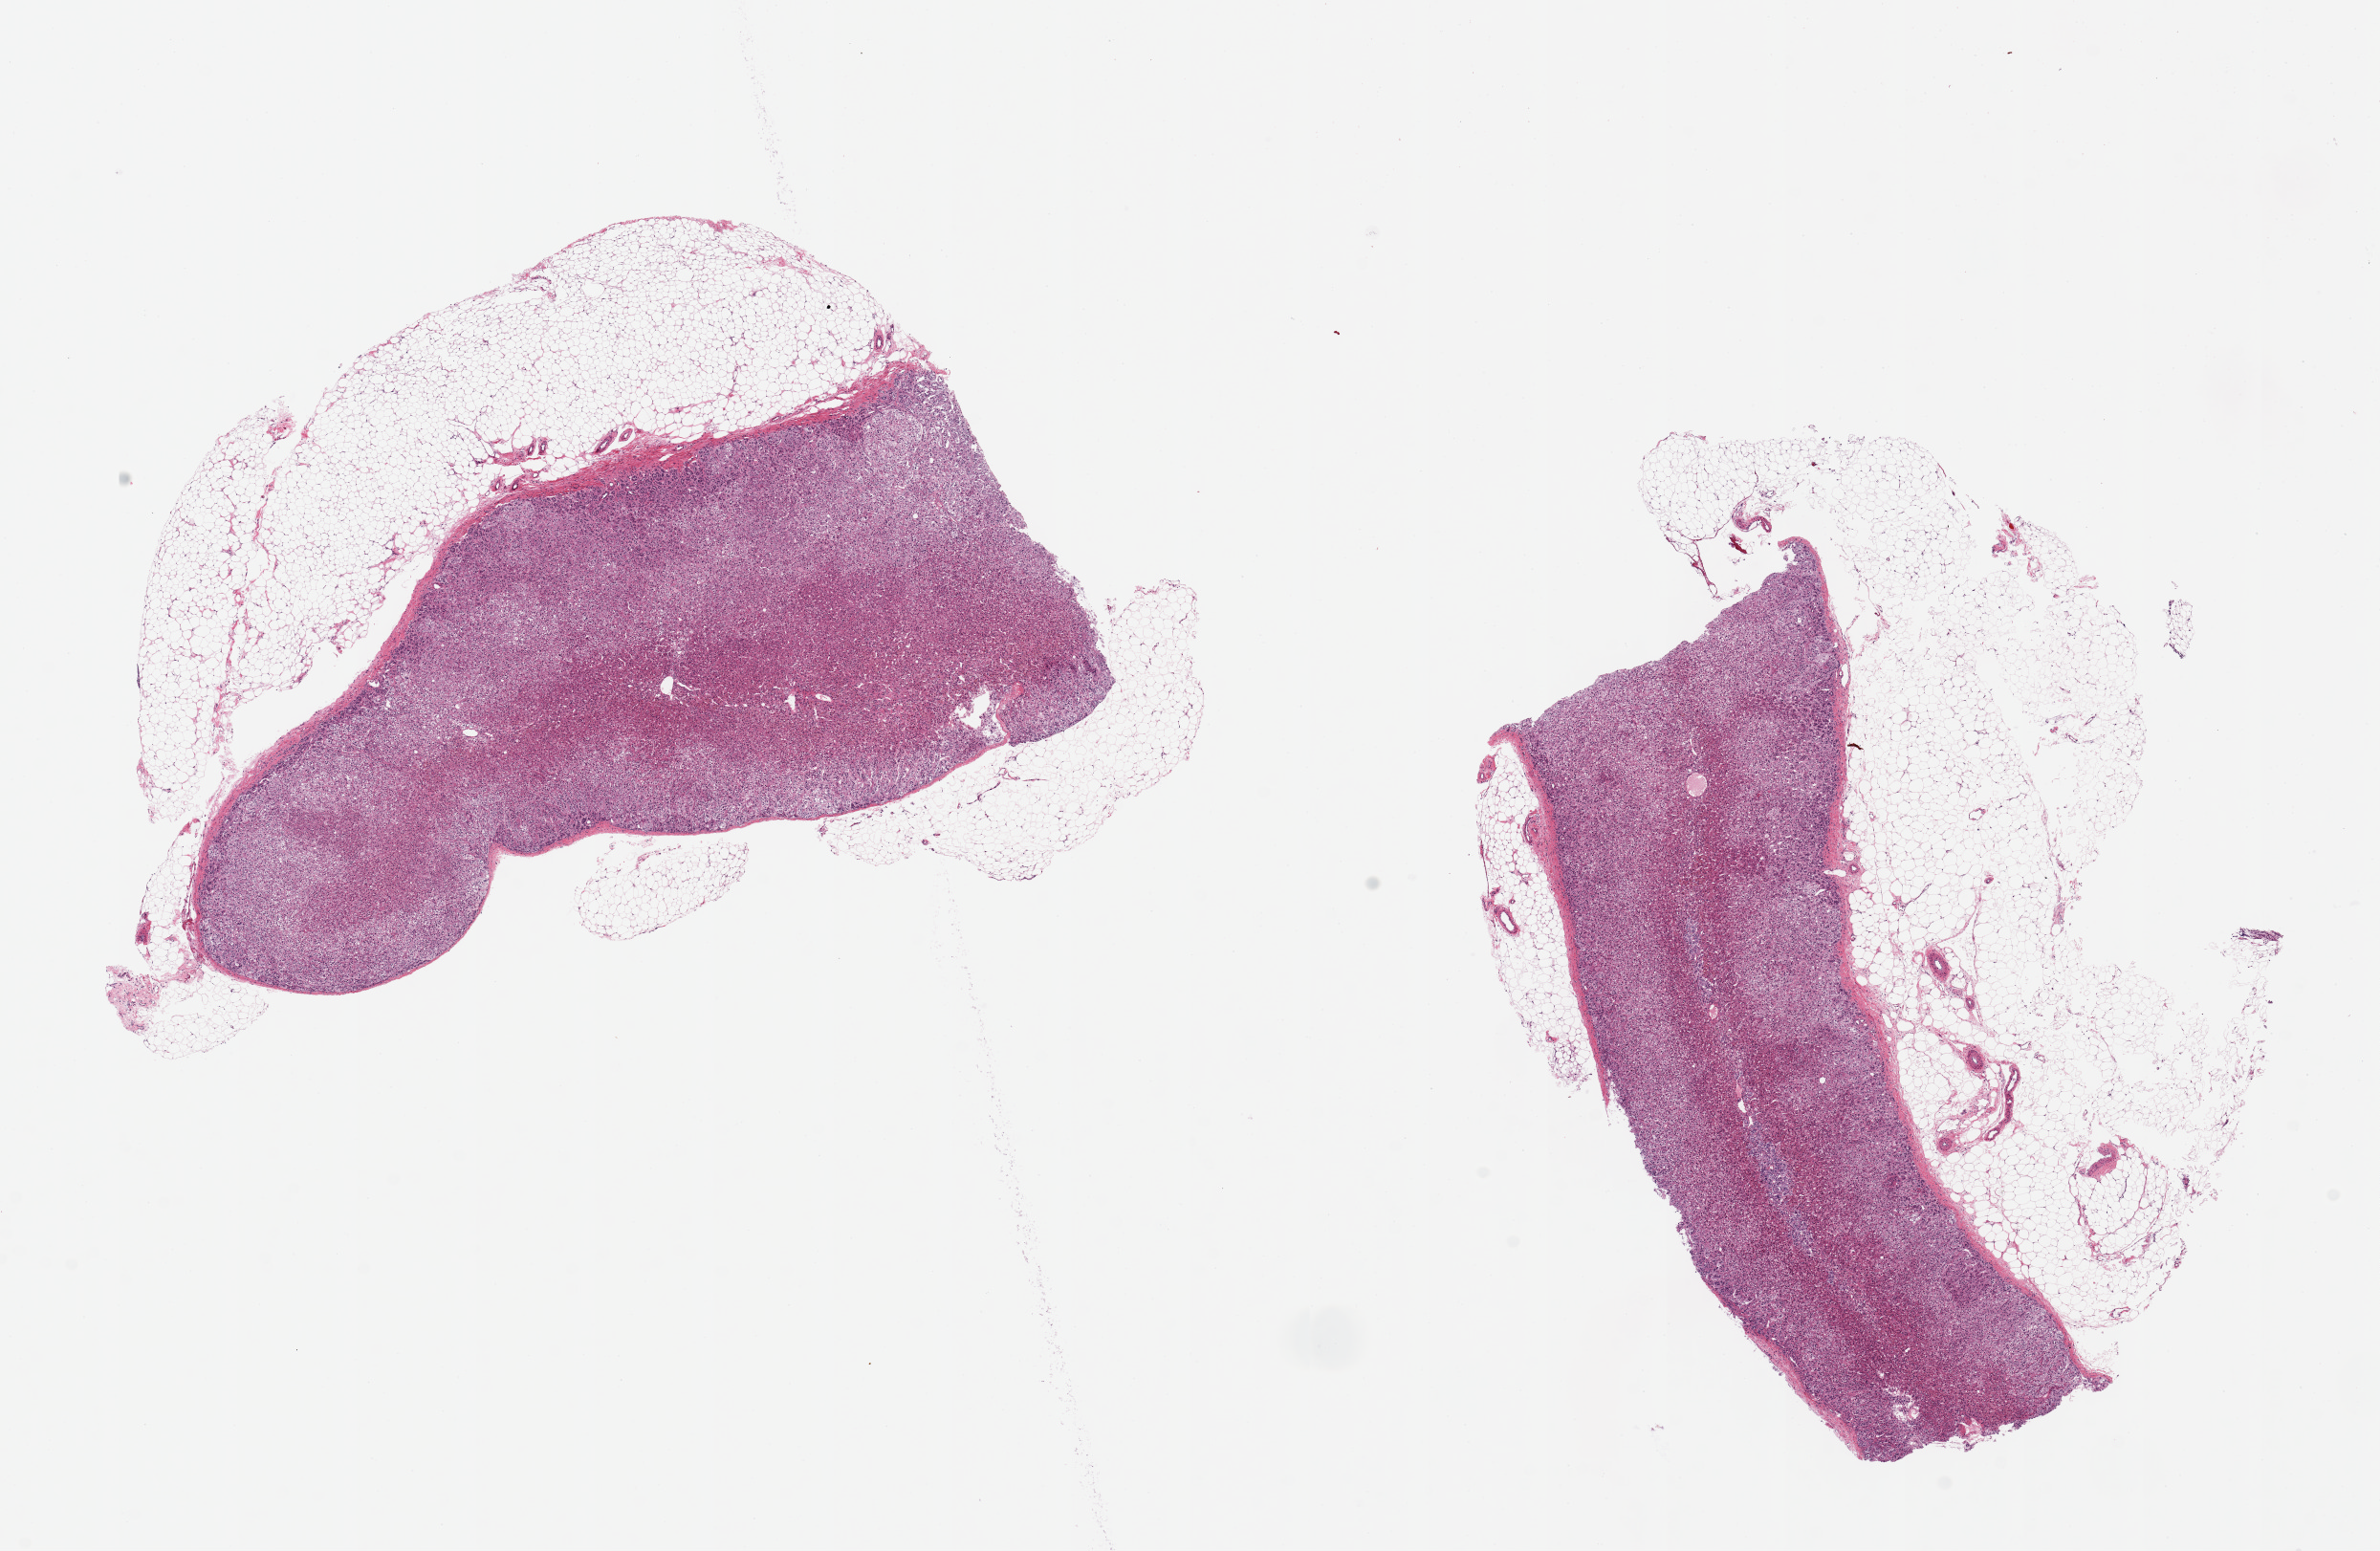
Whole-slide image, H&E stain — low-resolution overview of the scanned area, about 19.7 x 12.8 mm. PAXgene-fixed, paraffin-embedded tissue. Target tissue: adrenal gland. Donor tissue sample. Donor sex: male.
• review note (as recorded): 2 pieces, 9x6 & 9.5x6mm; good parenchyma, but 40-50% of aliquot is surrounding adipose tissue, up to 2.5 mm thick